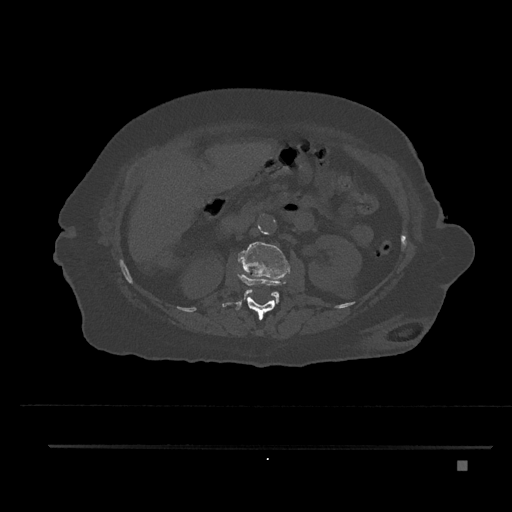
CT including the spine, one axial slice; position 207 of 797 along the scan axis; 120 kVp; bone window (W 1800 / L 400 HU); 0.5 mm slice thickness; 512 × 512 image matrix. Female patient, age 76 years. From the clinical record (not read from this slice): primary cancer: lung; vertebrae with lytic lesions (as recorded): T11, L3.
Structures marked on this image (semi-automatically segmented with operator editing):
- L1 vertebra: bounding box [x1, y1, x2, y2] px = [222, 272, 286, 320]
- L2 vertebra: [238, 242, 290, 304]